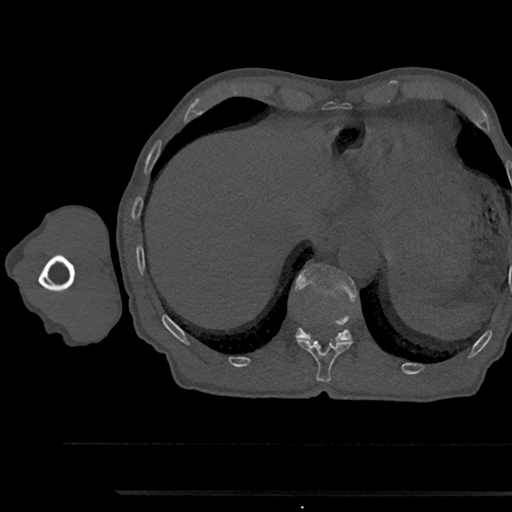
CT including the spine, one axial slice. Slice 756 of 797 in the series (ordered by position). Reconstruction kernel Br40s/3. 120 kVp. Bone window (W 1800 / L 400 HU). 0.5 mm slice thickness. 512 × 512 image matrix. Patient: male, 79 years. From the clinical record (not read from this slice): primary cancer: prostate.
Outlined on this slice (semi-automatic segmentation, software-assisted and operator-edited):
- T11 vertebra: bounding box <297,339,352,382> (left, top, right, bottom; pixels)
- T12 vertebra: <293,264,358,342>